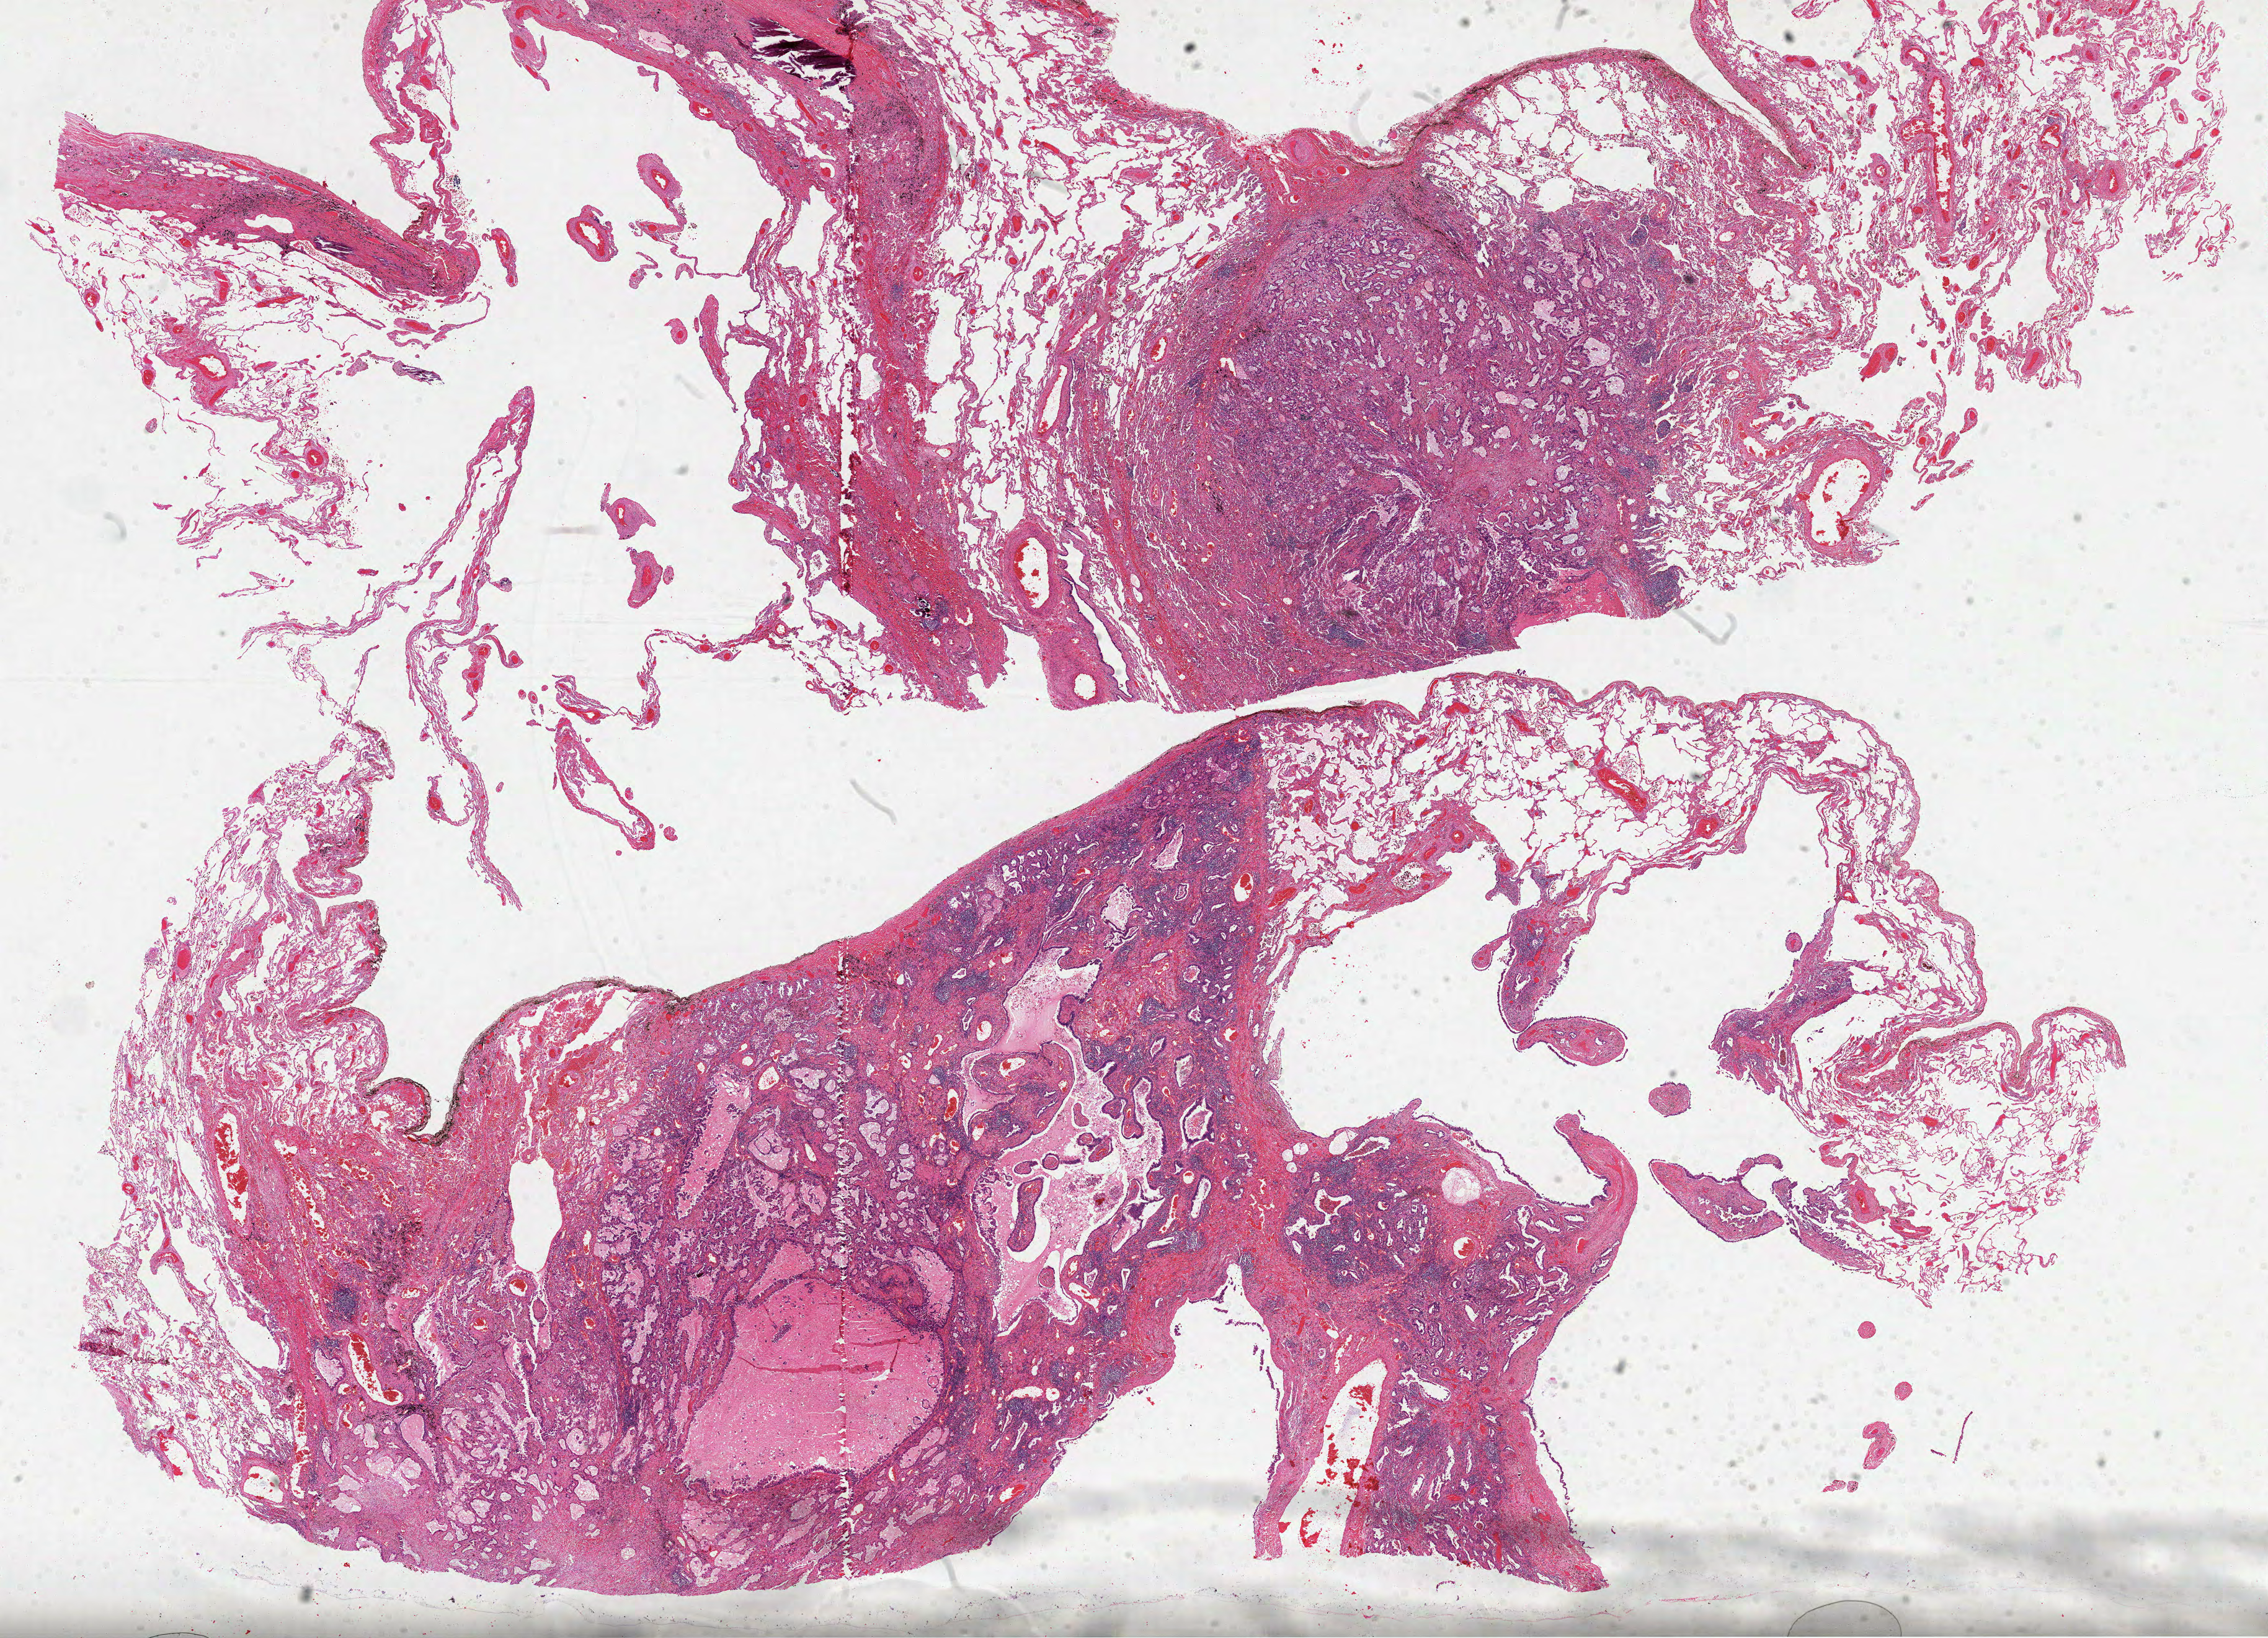
Digitized H&E-stained tissue section (whole slide), whole scanned area (about 29.5 x 21.3 mm, from a 40x scan) shown as a low-resolution overview, formalin-fixed paraffin-embedded (FFPE) diagnostic section, primary tumour sample from the lung. Male, age 71 years at initial diagnosis.
Histologic diagnosis: Adenocarcinoma with mixed subtypes. AJCC pathologic stage: IIB (6th edition).